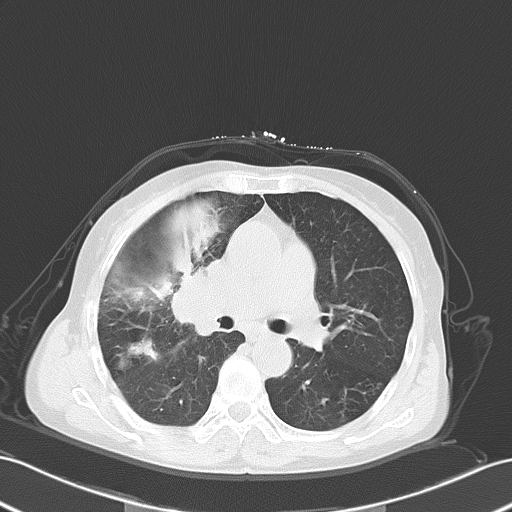
Chest CT, one axial slice; slice 32 of 55 in the series (ordered by position); 120 kVp; lung window (W 1500 / L -600 HU); 512 × 512 image matrix. Patient: female, 67 years. Case-level facts recorded for this patient, not image findings: clinical TNM (as recorded): T2a N3 M0; histopathological grade: G3.
Structures marked on this image (rectangle marked by the reading radiologist):
- lung tumour (recorded histology: small cell carcinoma): bounding box (x1, y1, x2, y2) in pixels: (165, 259, 228, 336)